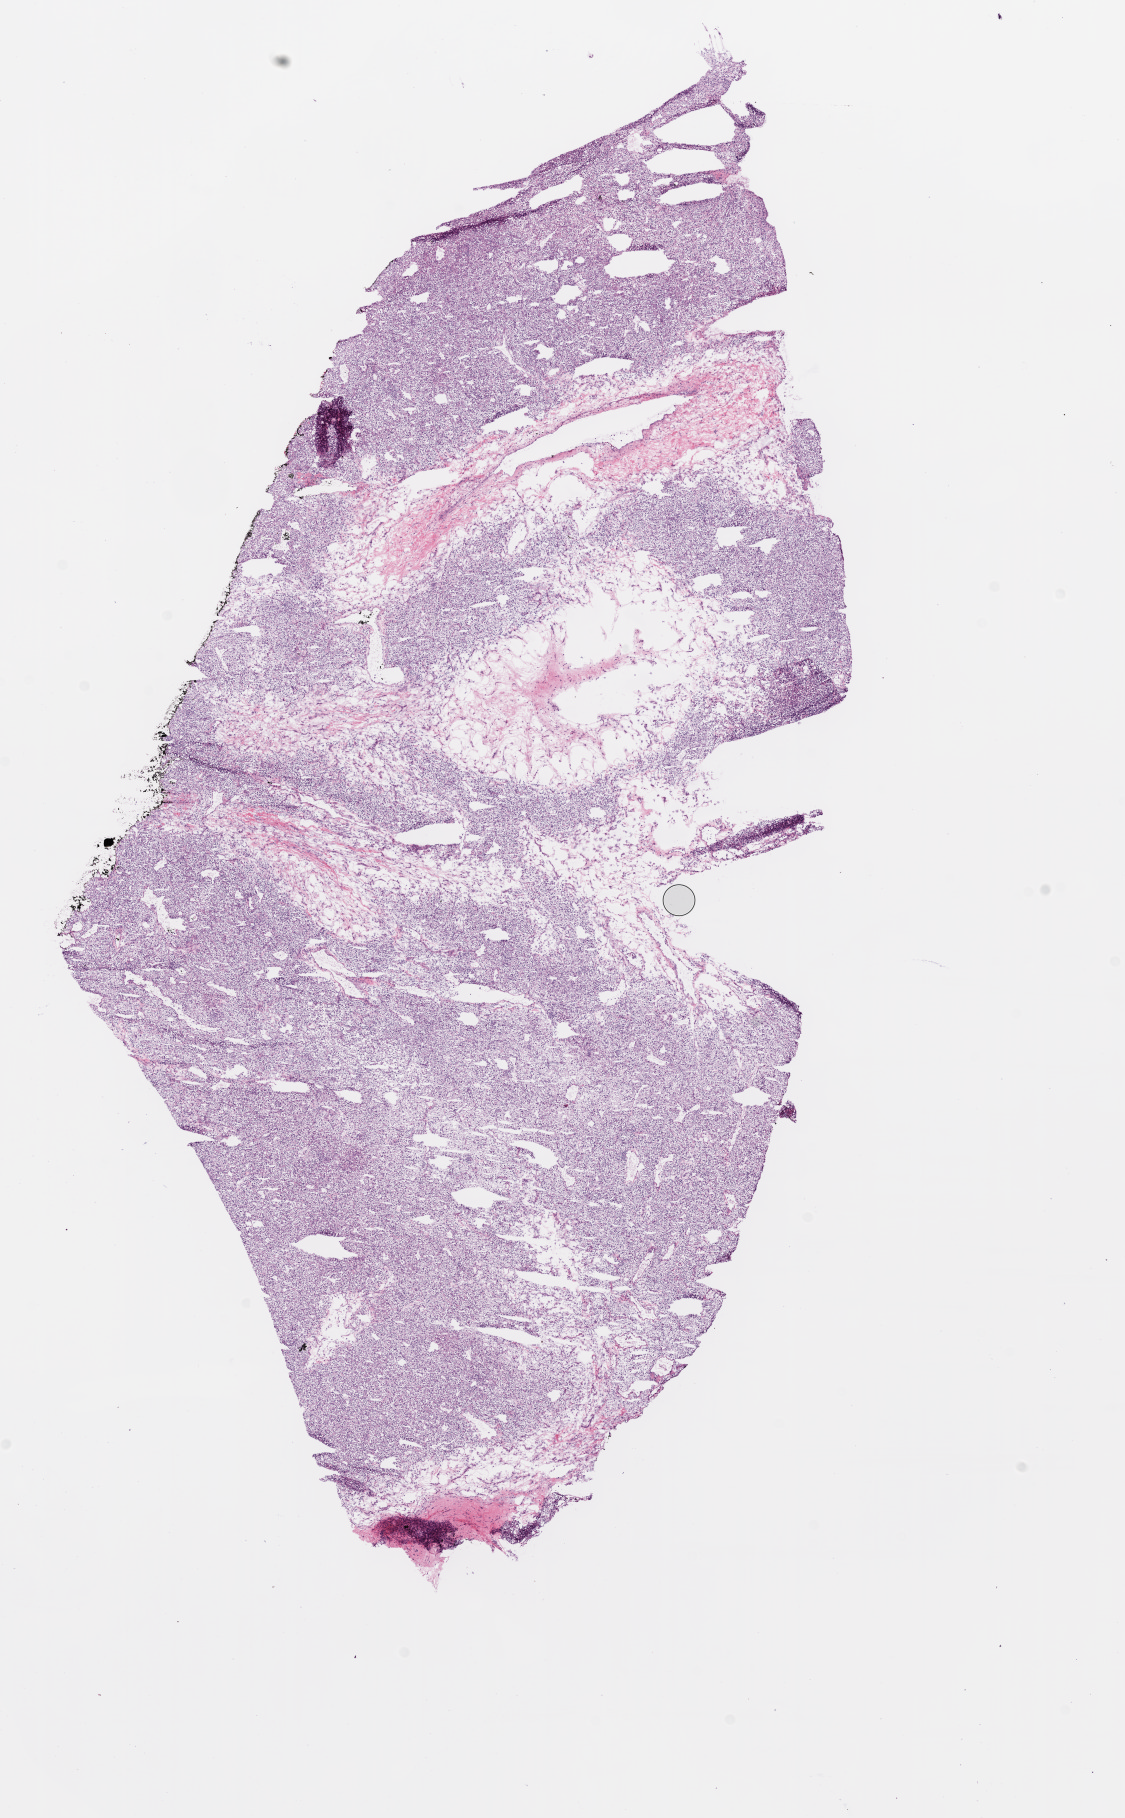
H&E whole-slide image — a low-resolution overview of the entire scanned area, about 9.0 x 14.6 mm (slide scanned at 20x), frozen section from the top of the tissue portion, kidney, primary tumour sample. Patient: male, age at initial diagnosis 75 years. Histologic grade: G2 (moderately differentiated). Pathologist review of this section (percent, as recorded): tumour cells 85%, tumour nuclei 85%, normal cells 0%, stromal cells 15%, necrosis 0%.
- AJCC pathologic stage: I
- histologic diagnosis: Clear cell adenocarcinoma, NOS